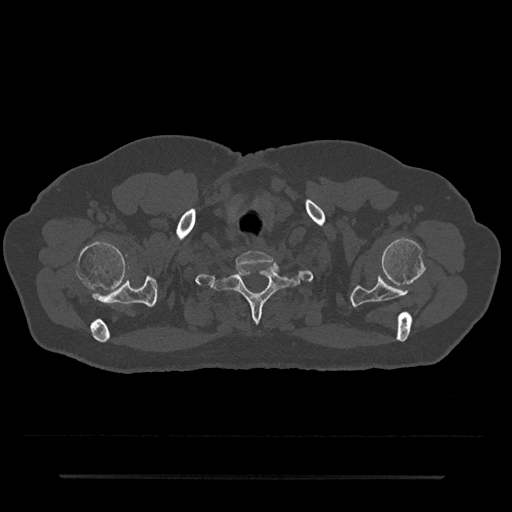
CT including the spine, one axial slice. Slice 644 of 797 in the series (ordered by position). Reconstruction kernel Br40s/3. Bone window (W 1800 / L 400 HU). 512 × 512 image matrix, field of view 437 × 437 mm. Patient: male, 69 years. From the clinical record (not read from this slice): primary cancer: prostate.
Annotated regions visible in this slice (semi-automatic segmentation, software-assisted and operator-edited):
- T1 vertebra: bounding box [x1, y1, x2, y2] px = [211, 265, 302, 322]